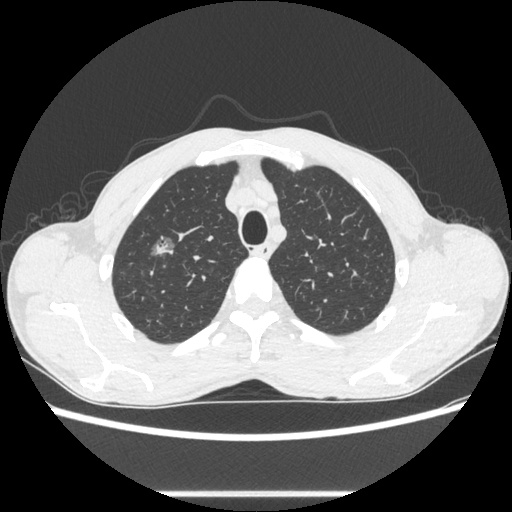
Chest CT, one axial slice. Slice 484 of 600 in the series (ordered by position). 100 kVp. Lung window (W 1500 / L -600 HU). 512 × 512 image matrix, field of view 357 × 357 mm. Patient: male, 54 years. Case-level facts recorded for this patient, not image findings: clinical TNM (as recorded): T1a N0 M0.
Structures marked on this image (rectangle marked by the reading radiologist):
- lung tumour (recorded histology: adenocarcinoma): box from (x=146, y=226) to (x=181, y=268) px